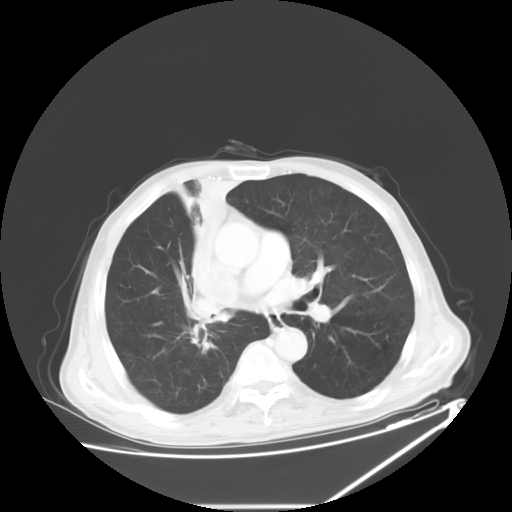
Chest CT, one axial slice. Slice 35 of 60 in the series (ordered by position). Reconstruction kernel STANDARD. 120 kVp. Lung window (W 1500 / L -600 HU). 5 mm slice thickness. 512 × 512 image matrix, field of view 410 × 410 mm. Male patient, age 73 years. From the clinical record (not read from this slice): clinical TNM (as recorded): T2a N1 M0.
Annotated regions visible in this slice (bounding box drawn by a radiologist):
- lung tumour (recorded histology: squamous cell carcinoma): box from (x=174, y=166) to (x=250, y=330) px